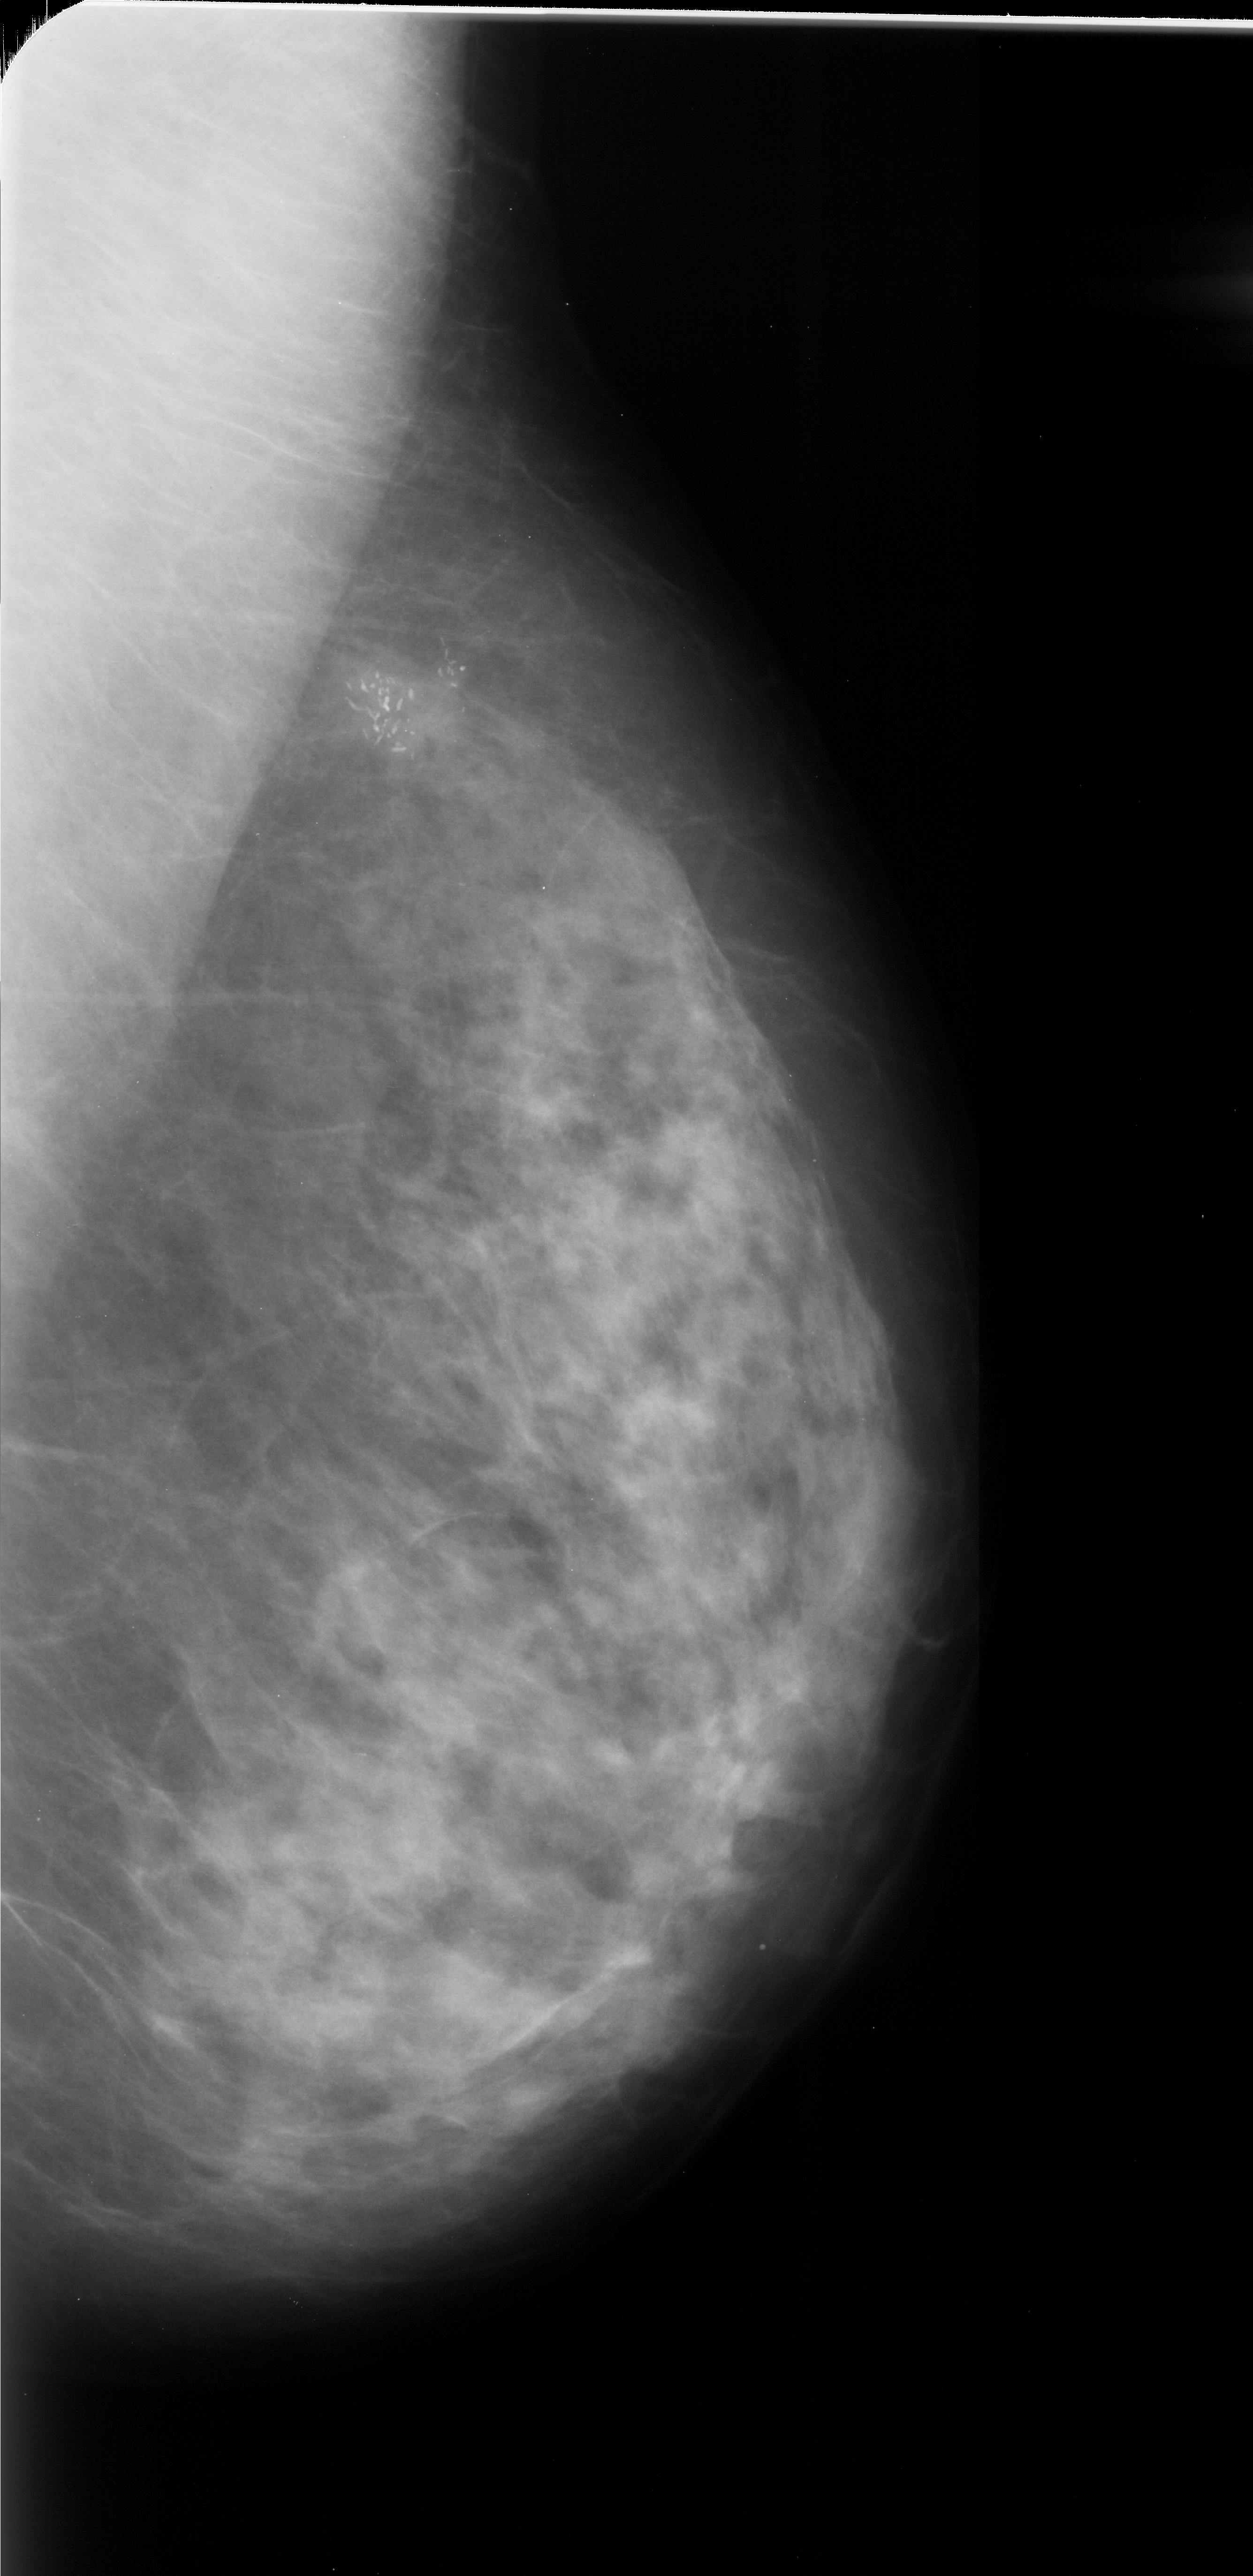
Scanned film-screen mammogram; right breast; MLO view; BI-RADS breast density category 3 (scale 1–4).
Abnormality record for this image: calcifications, morphology fine linear branching, distribution clustered; BI-RADS assessment category 5; subtlety rating 5 on a 1 (subtle) to 5 (obvious) scale; pathology result (as recorded, not read from the image): malignant.